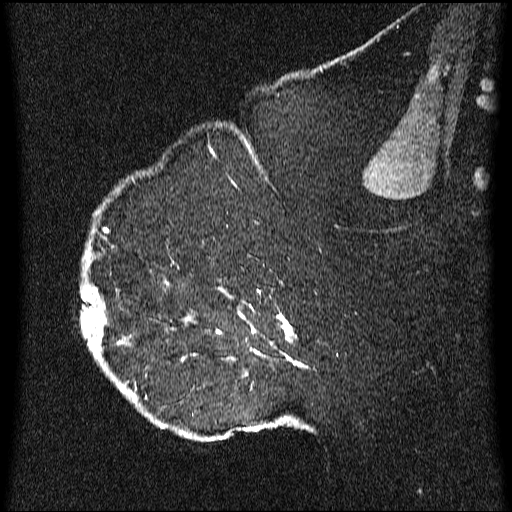
Breast MRI (dynamic contrast-enhanced), one sagittal slice; slice 46 of 64 in the series (ordered by position); dynamic contrast-enhanced series, image 2 of 3 at this slice position (ordered by acquisition); 1.5 T; TE 4.2 ms, TR 9.1 ms; 512 × 512 image matrix, field of view 180 × 180 mm. Patient: female, 52 years.
Annotated regions visible in this slice (semi-automatic segmentation, software-assisted and operator-edited):
- analysis volume of interest (the breast-tissue region the enhancement analysis was run in; not a lesion): bounding box <81,203,331,438> (left, top, right, bottom; pixels)
- tumour enhancement mask (voxels above the 70 % enhancement threshold inside the analysis volume of interest): <81,229,309,436>